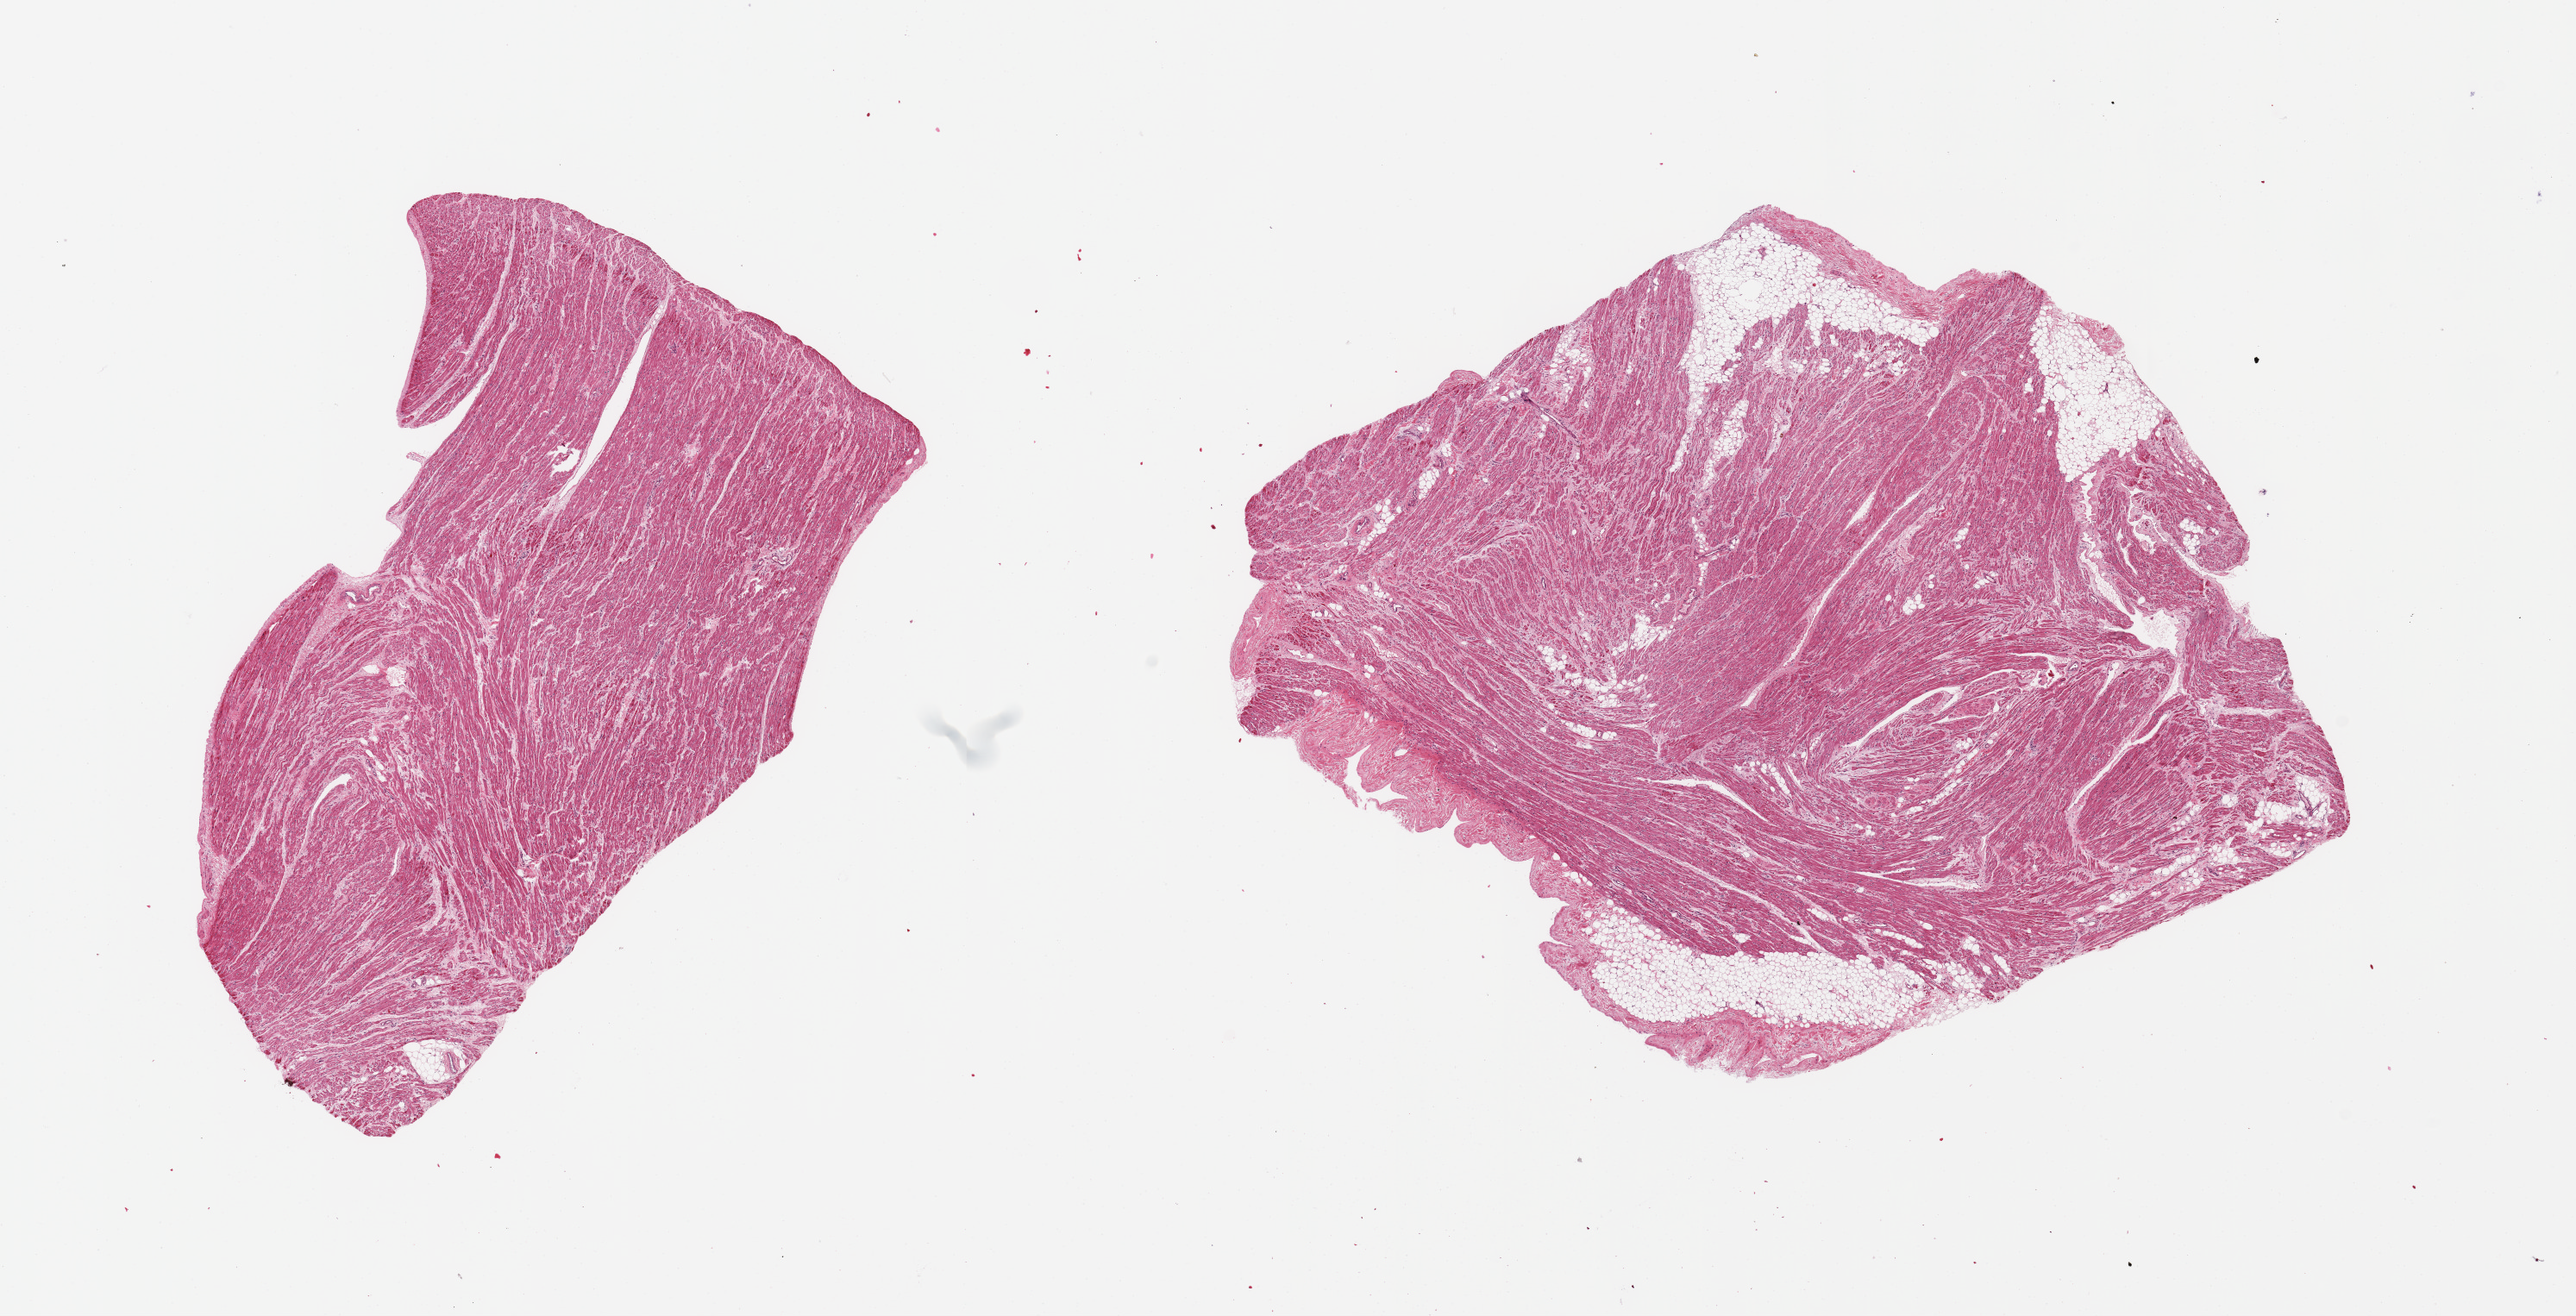
Whole-slide image, haematoxylin and eosin stain, shown as a low-resolution overview of the whole scanned area (about 23.6 x 12.1 mm); PAXgene-fixed paraffin-embedded (PFPE) section; sampled site (target tissue): auricular appendage; tissue donor sample. Donor sex: female.
Reviewer comment on this tissue sample: 2 pieces; one contains ~15% fat.